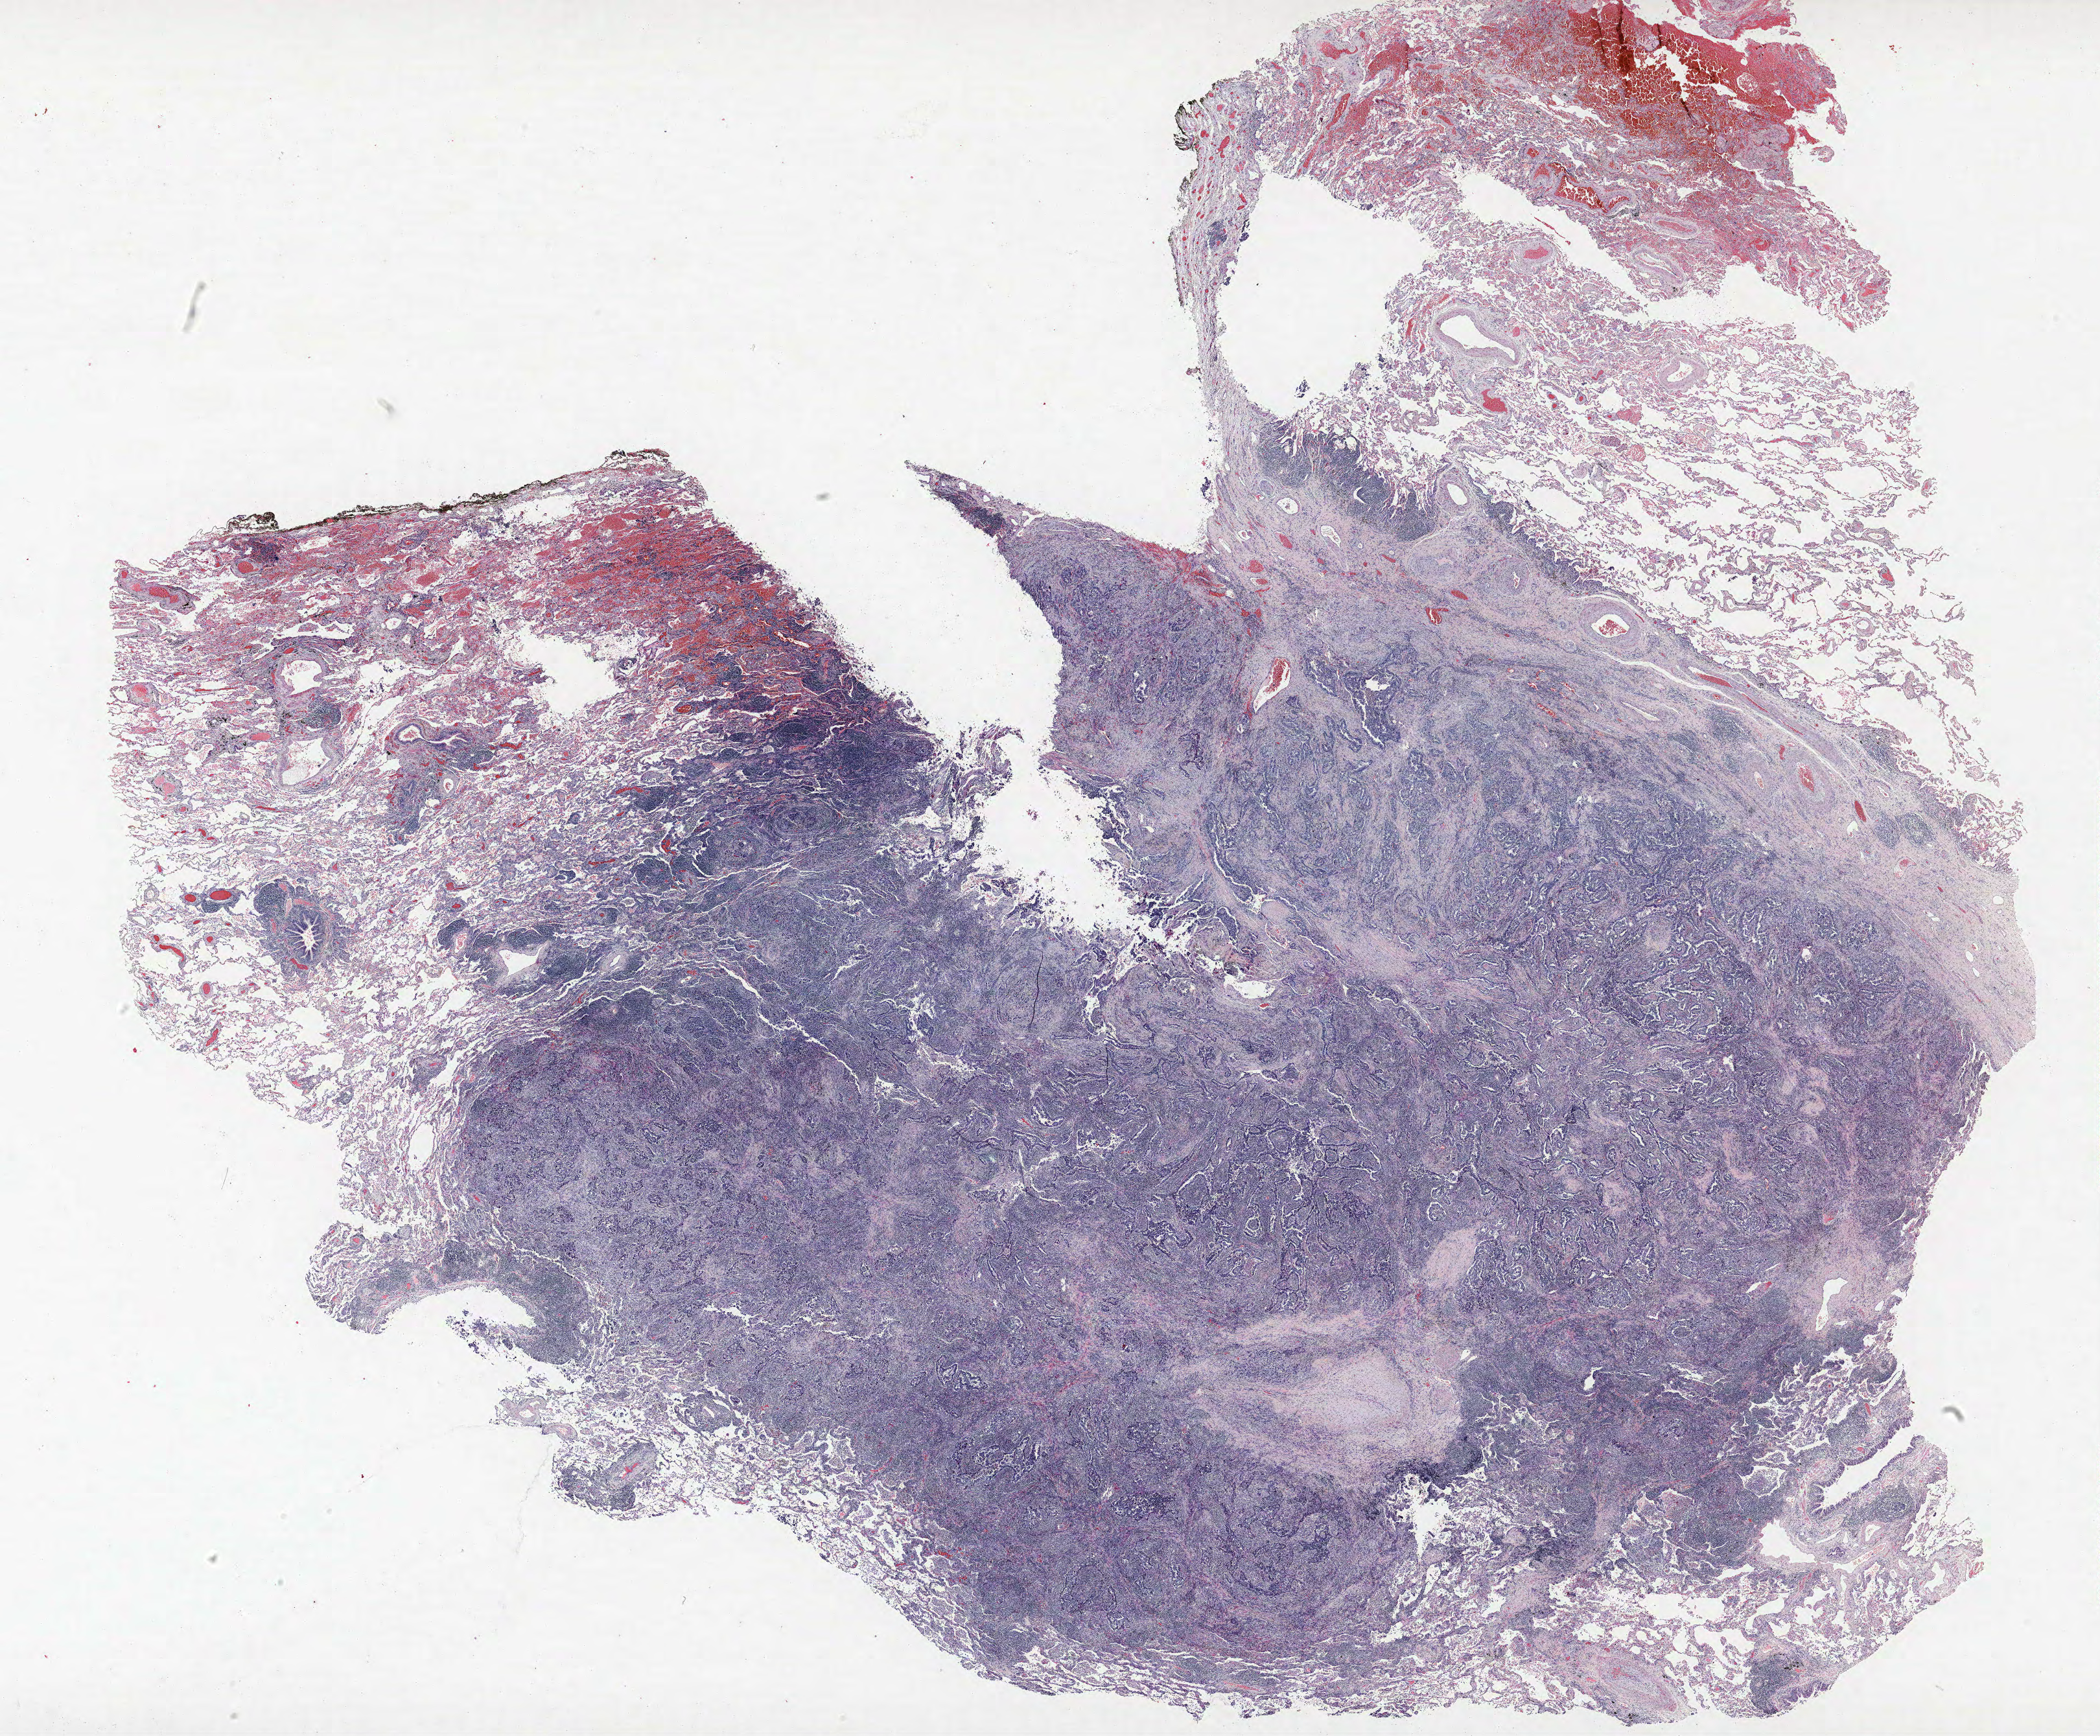
H&E-stained whole-slide image, a low-resolution overview of the entire scanned area, about 25.9 x 21.4 mm (from a 40x scan); formalin-fixed paraffin-embedded (FFPE) section; lung tissue. Male patient, aged 73 at enrolment. Current smoker at enrolment. Grade: poorly differentiated (G3).
* primary tumour location (clinical record): right upper lobe
* stage (AJCC 6th edition): IA
* participant's lung-cancer diagnosis: Adenocarcinoma, NOS
* tumour size (pathology): 22 mm